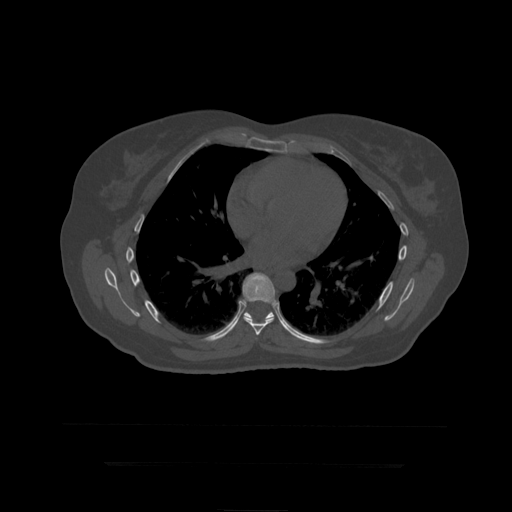
CT including the spine, one axial slice; position 275 of 399 along the scan axis; reconstruction kernel STANDARD; 120 kVp; bone window (W 1800 / L 400 HU); 512 × 512 image matrix, field of view 450 × 450 mm. Patient age 41 years. From the clinical record (not read from this slice): primary cancer: breast.
Annotated regions visible in this slice (semi-automatically segmented with operator editing):
- T8 vertebra: bounding box (x1, y1, x2, y2) in pixels: (243, 273, 276, 336)
- T9 vertebra: (228, 285, 294, 336)